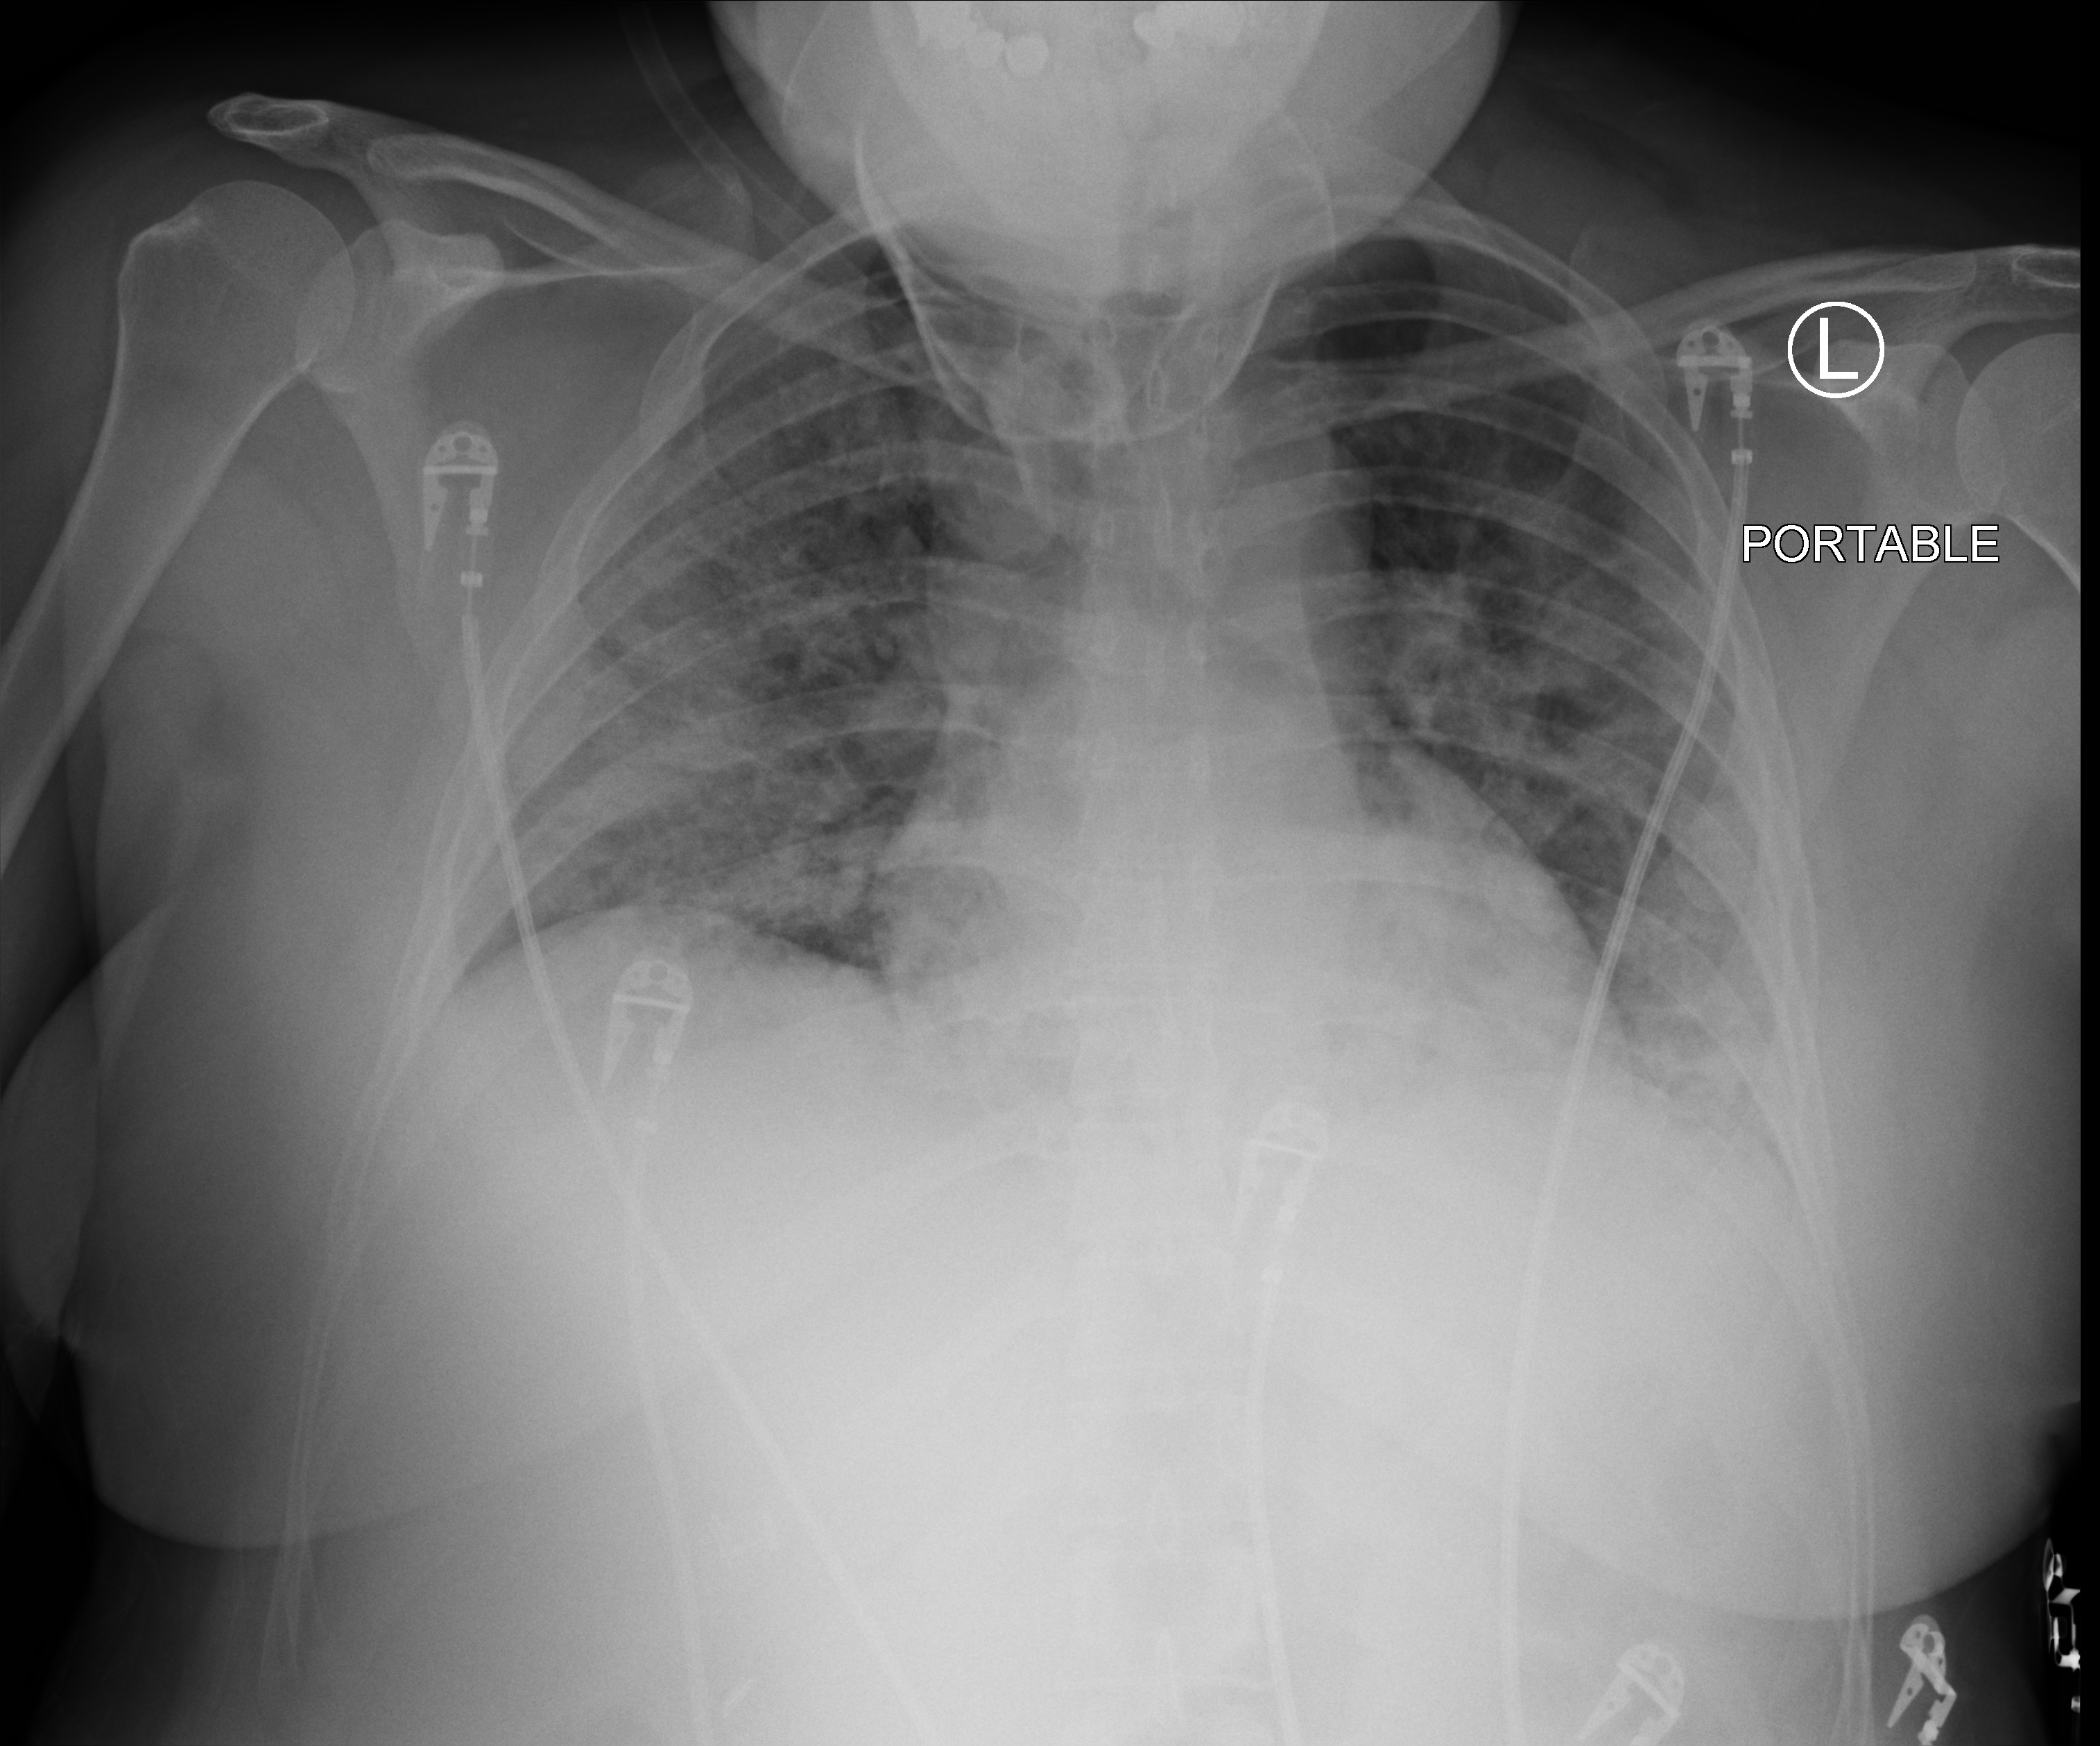
Portable chest radiograph; anteroposterior (AP) projection. Patient hospitalised with COVID-19; female, aged 18–59 years.
Admission-level facts for this patient (not findings on this image; timing relative to this image not recorded):
- admitted to intensive care during this hospital stay: no
- mechanically ventilated during this hospital stay: no
- hypertension (admission record): no